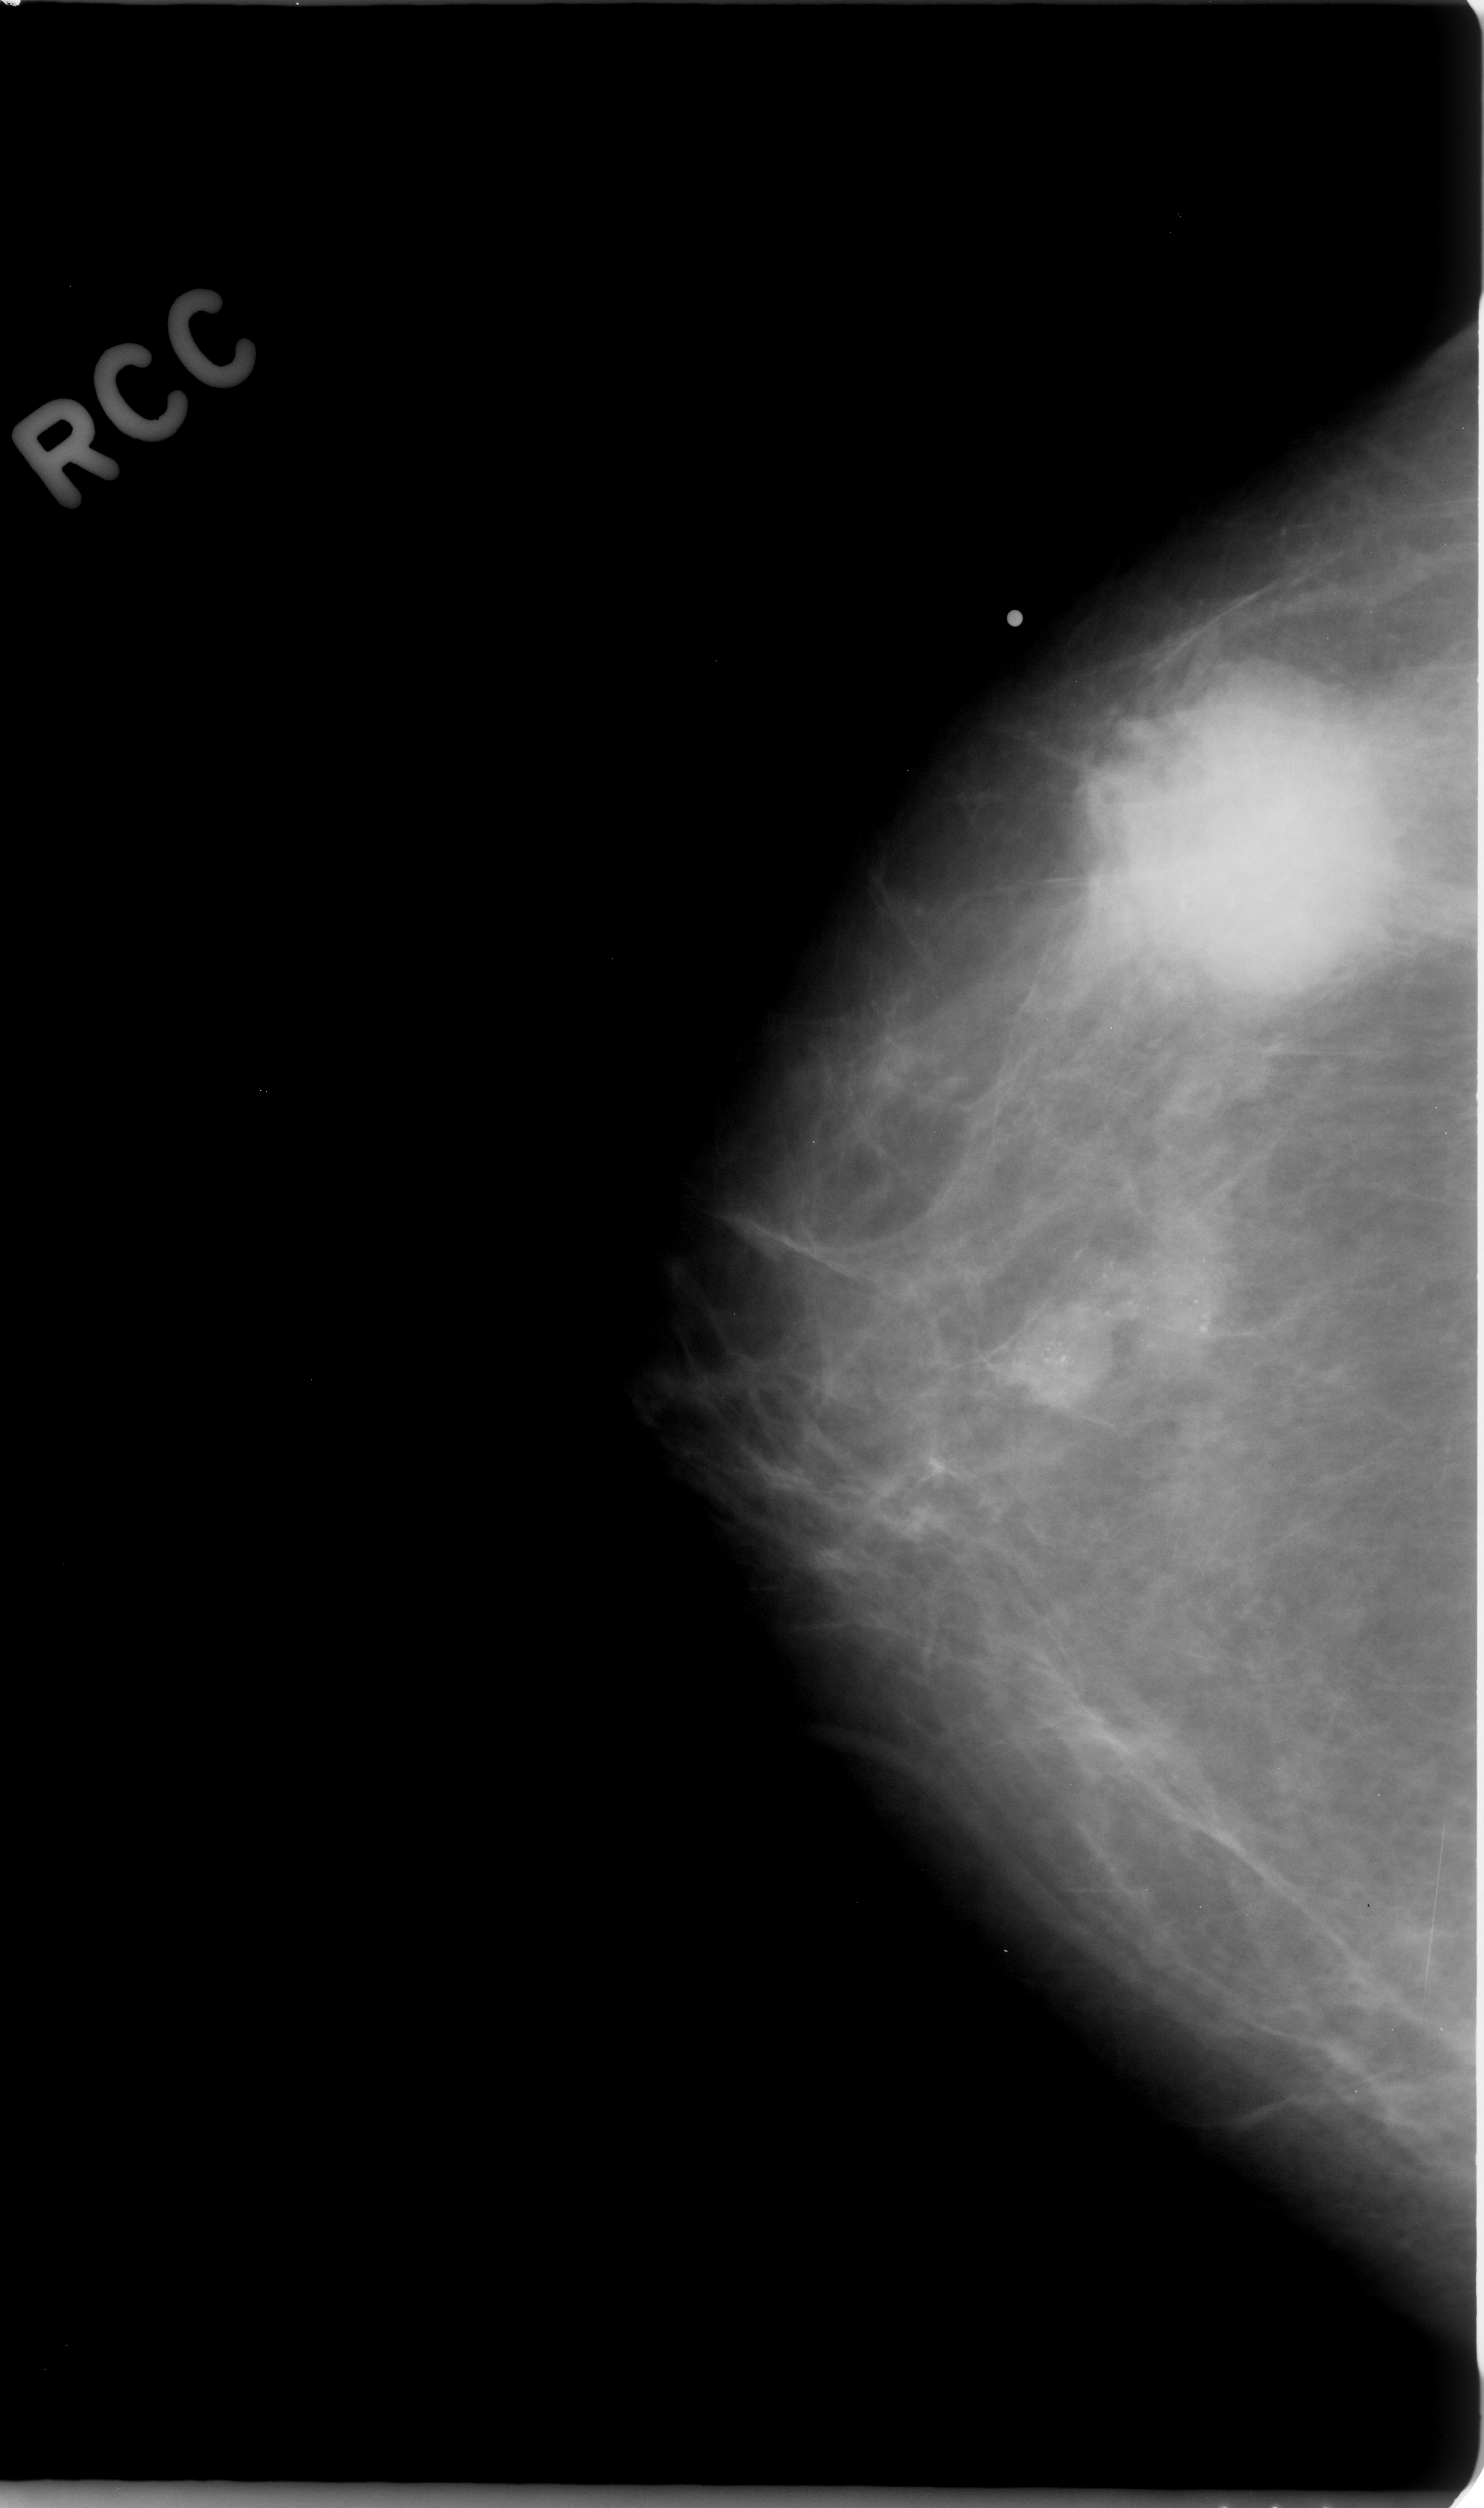
Digitized screen-film mammogram; right breast; craniocaudal (CC) view.
Abnormality record for this image: calcifications, morphology amorphous, distribution clustered; BI-RADS assessment category 5; subtlety rating 5 on a 1 (subtle) to 5 (obvious) scale; pathology result (as recorded, not read from the image): malignant.